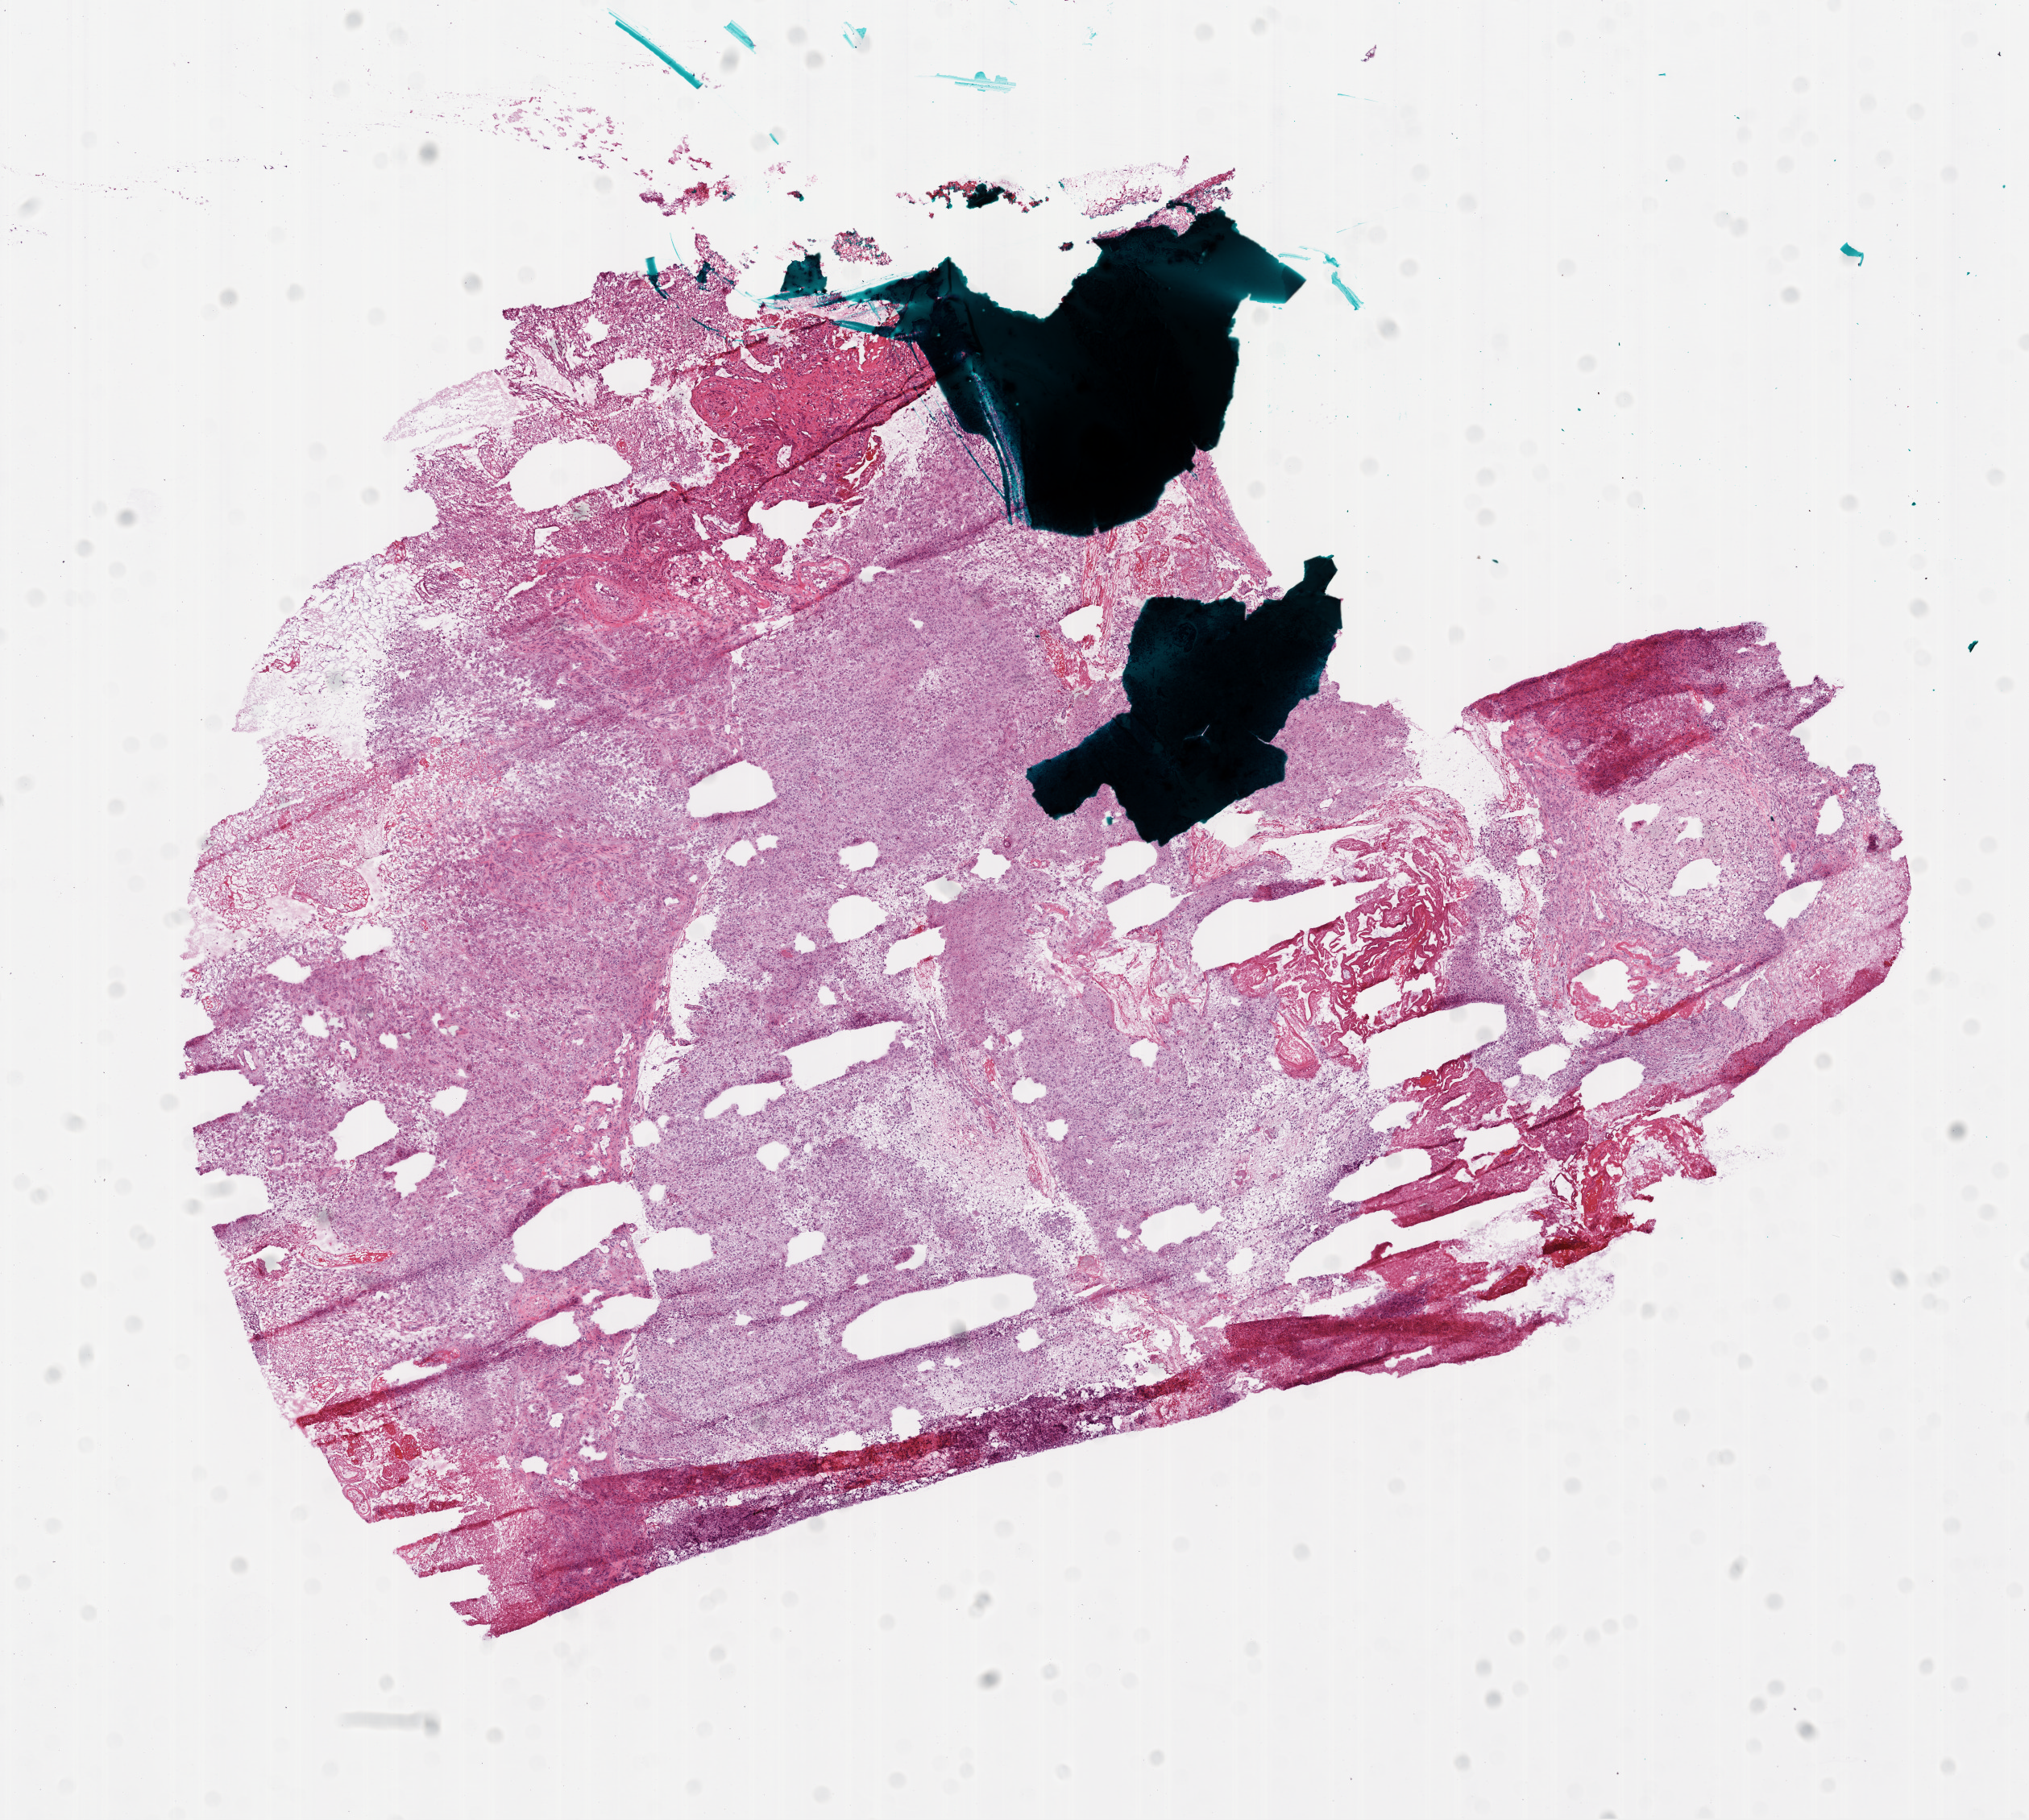
Digitized H&E tissue section (whole slide), low-resolution overview of the scanned area, about 10.2 x 9.1 mm (from a 20x scan); frozen section; sample: primary tumour, brain. Male, age 43 years at initial diagnosis. Slide review estimates, as recorded: tumour cells 80%, tumour nuclei 90%, normal cells 0%, stromal cells 5%, necrosis 15%.
- diagnosis: Glioblastoma